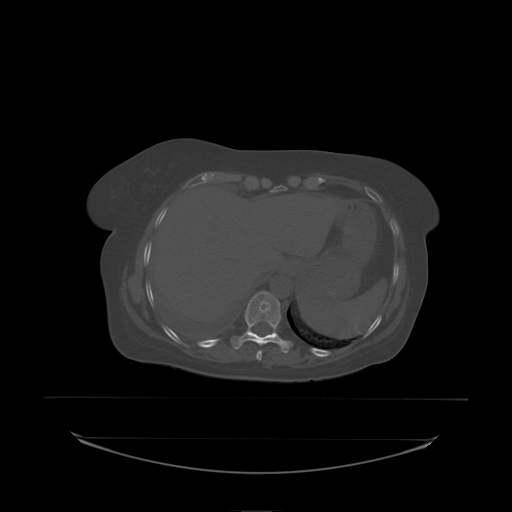
CT including the spine, one axial slice; slice 114 of 242 in the series (ordered by position); bone window (W 1800 / L 400 HU); 2.5 mm slice thickness; 512 × 512 image matrix. Patient: female, 53 years. Case-level facts recorded for this patient, not image findings: primary cancer: lung; vertebrae with lytic lesions (as recorded): T7, L1.
Outlined on this slice (semi-automatic segmentation, software-assisted and operator-edited):
- T10 vertebra: bounding box <242,292,282,338> (left, top, right, bottom; pixels)